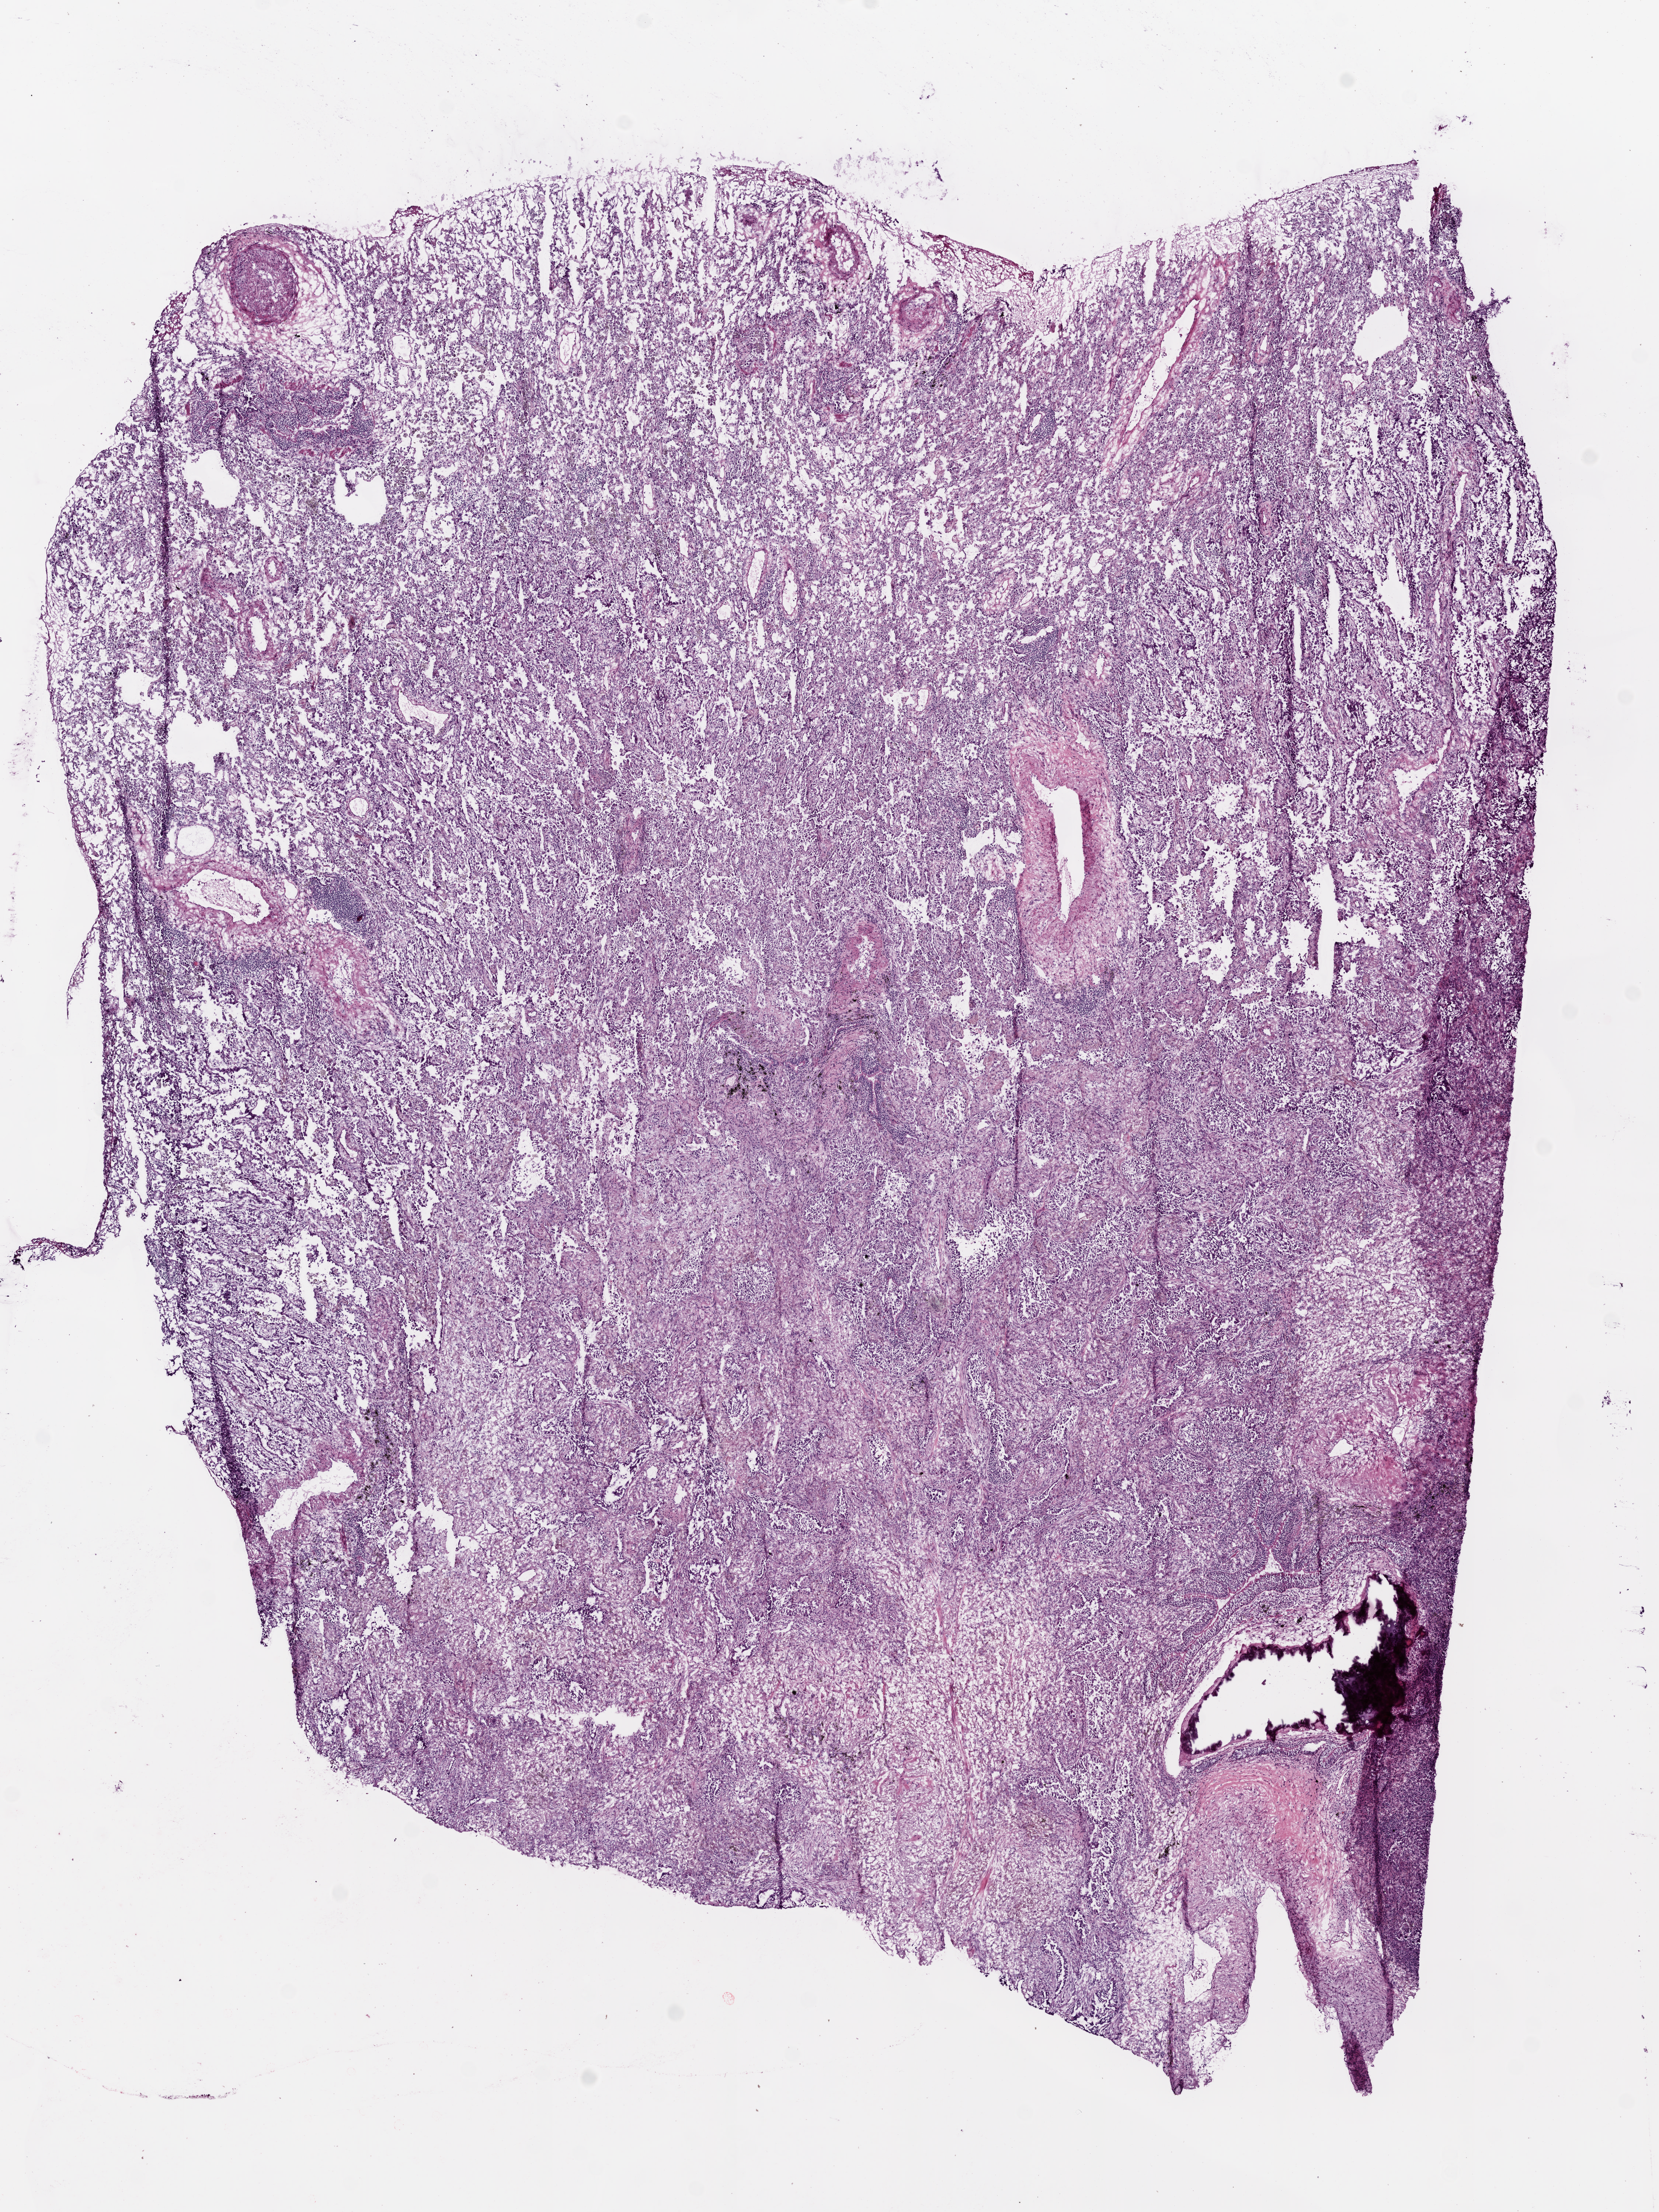
H&E-stained whole-slide image, shown as a low-resolution overview of the whole scanned area (about 9.0 x 12.0 mm, acquisition: 20x scan), frozen section, primary tumour sample from the lung. Female, age 59 years at initial diagnosis. Composition of this section per pathologist review: tumour cells 70%, tumour nuclei 70%, normal cells 20%, stromal cells 10%, necrosis 0%.
TNM: T2 N0 M0. Pathologic diagnosis: Adenocarcinoma with mixed subtypes (lower lobe, lung). AJCC pathologic stage: IB (6th edition).